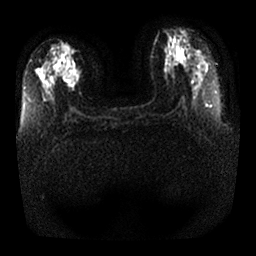
Breast MRI, one axial slice; slice 12 of 25 in the series (ordered by position); diffusion-weighted series; image 2 of 4 stored at this slice position (different b-values; order by instance number); 1.5 T; 4 mm slice thickness; 256 × 256 image matrix. Female patient.
Outlined on this slice (outlined manually by an expert reader):
- tumour on diffusion-weighted imaging: bounding box <62,46,80,81> (left, top, right, bottom; pixels)